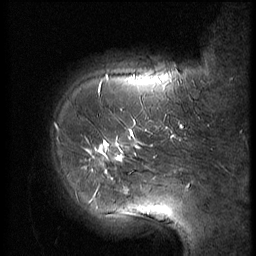
Breast MRI (dynamic contrast-enhanced), one sagittal slice. 3 images stored at this slice position (order not interpretable as contrast timing). 1.5 T. TE 4.2 ms, TR 9 ms. 2.5 mm slice thickness. 256 × 256 image matrix, field of view 180 × 180 mm. Female patient, age 61 years. From the clinical record (not read from this slice): setting: breast cancer imaged before/during neoadjuvant chemotherapy; receptor status: HR-positive, HER2-negative.
Annotated regions visible in this slice (semi-automatically segmented with operator editing):
- analysis volume of interest (the breast-tissue region the enhancement analysis was run in; not a lesion): bounding box (x1, y1, x2, y2) in pixels: (47, 89, 153, 191)
- tumour enhancement mask (voxels above the 140 % enhancement threshold inside the analysis volume of interest): (90, 130, 152, 191)